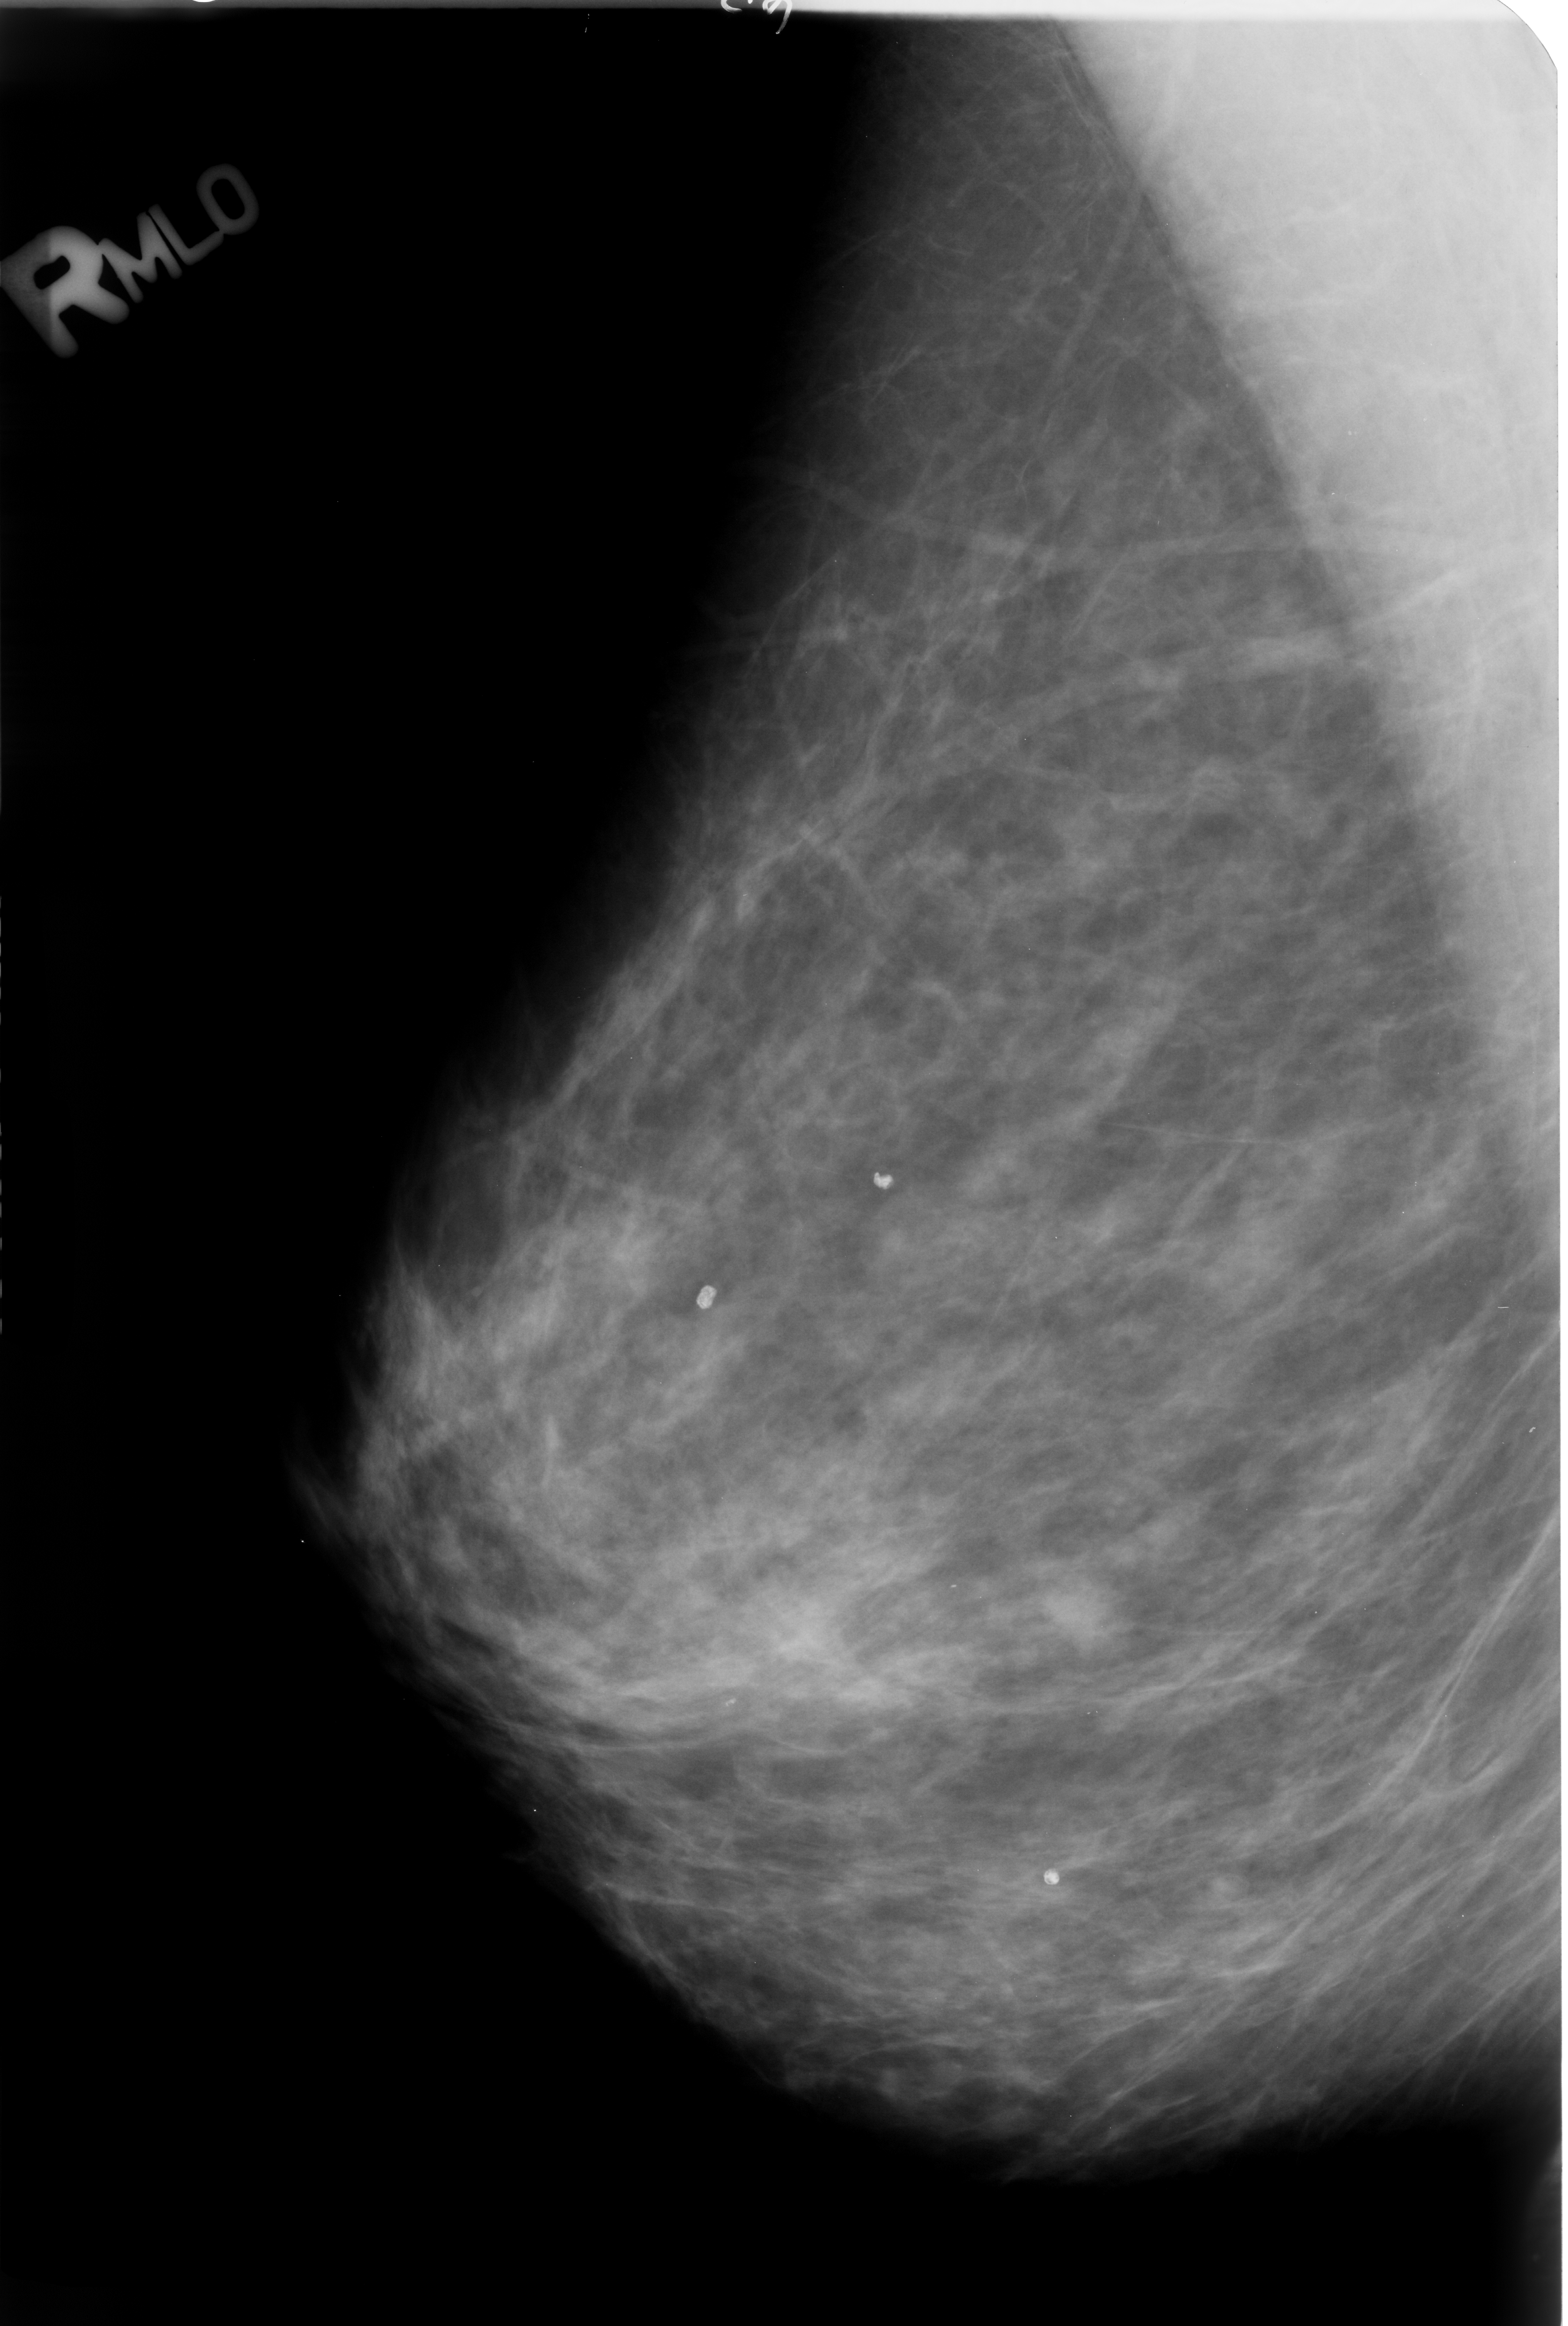
Mammogram (digitized film); right breast; MLO view.
Marked findings (only marked abnormalities are described; nothing is implied about the rest of the image): Finding 1 of 3: calcifications, morphology coarse / round and regular / lucent center; BI-RADS assessment category 2; subtlety rating 5 on a 1 (subtle) to 5 (obvious) scale; benign without callback (not worked up further). Finding 2 of 3: calcifications, morphology coarse / round and regular / lucent center; BI-RADS assessment category 2; benign without callback (not worked up further). Finding 3 of 3: calcifications, morphology coarse / round and regular / lucent center; BI-RADS assessment category 2; benign; no additional work-up was recommended (benign without callback).